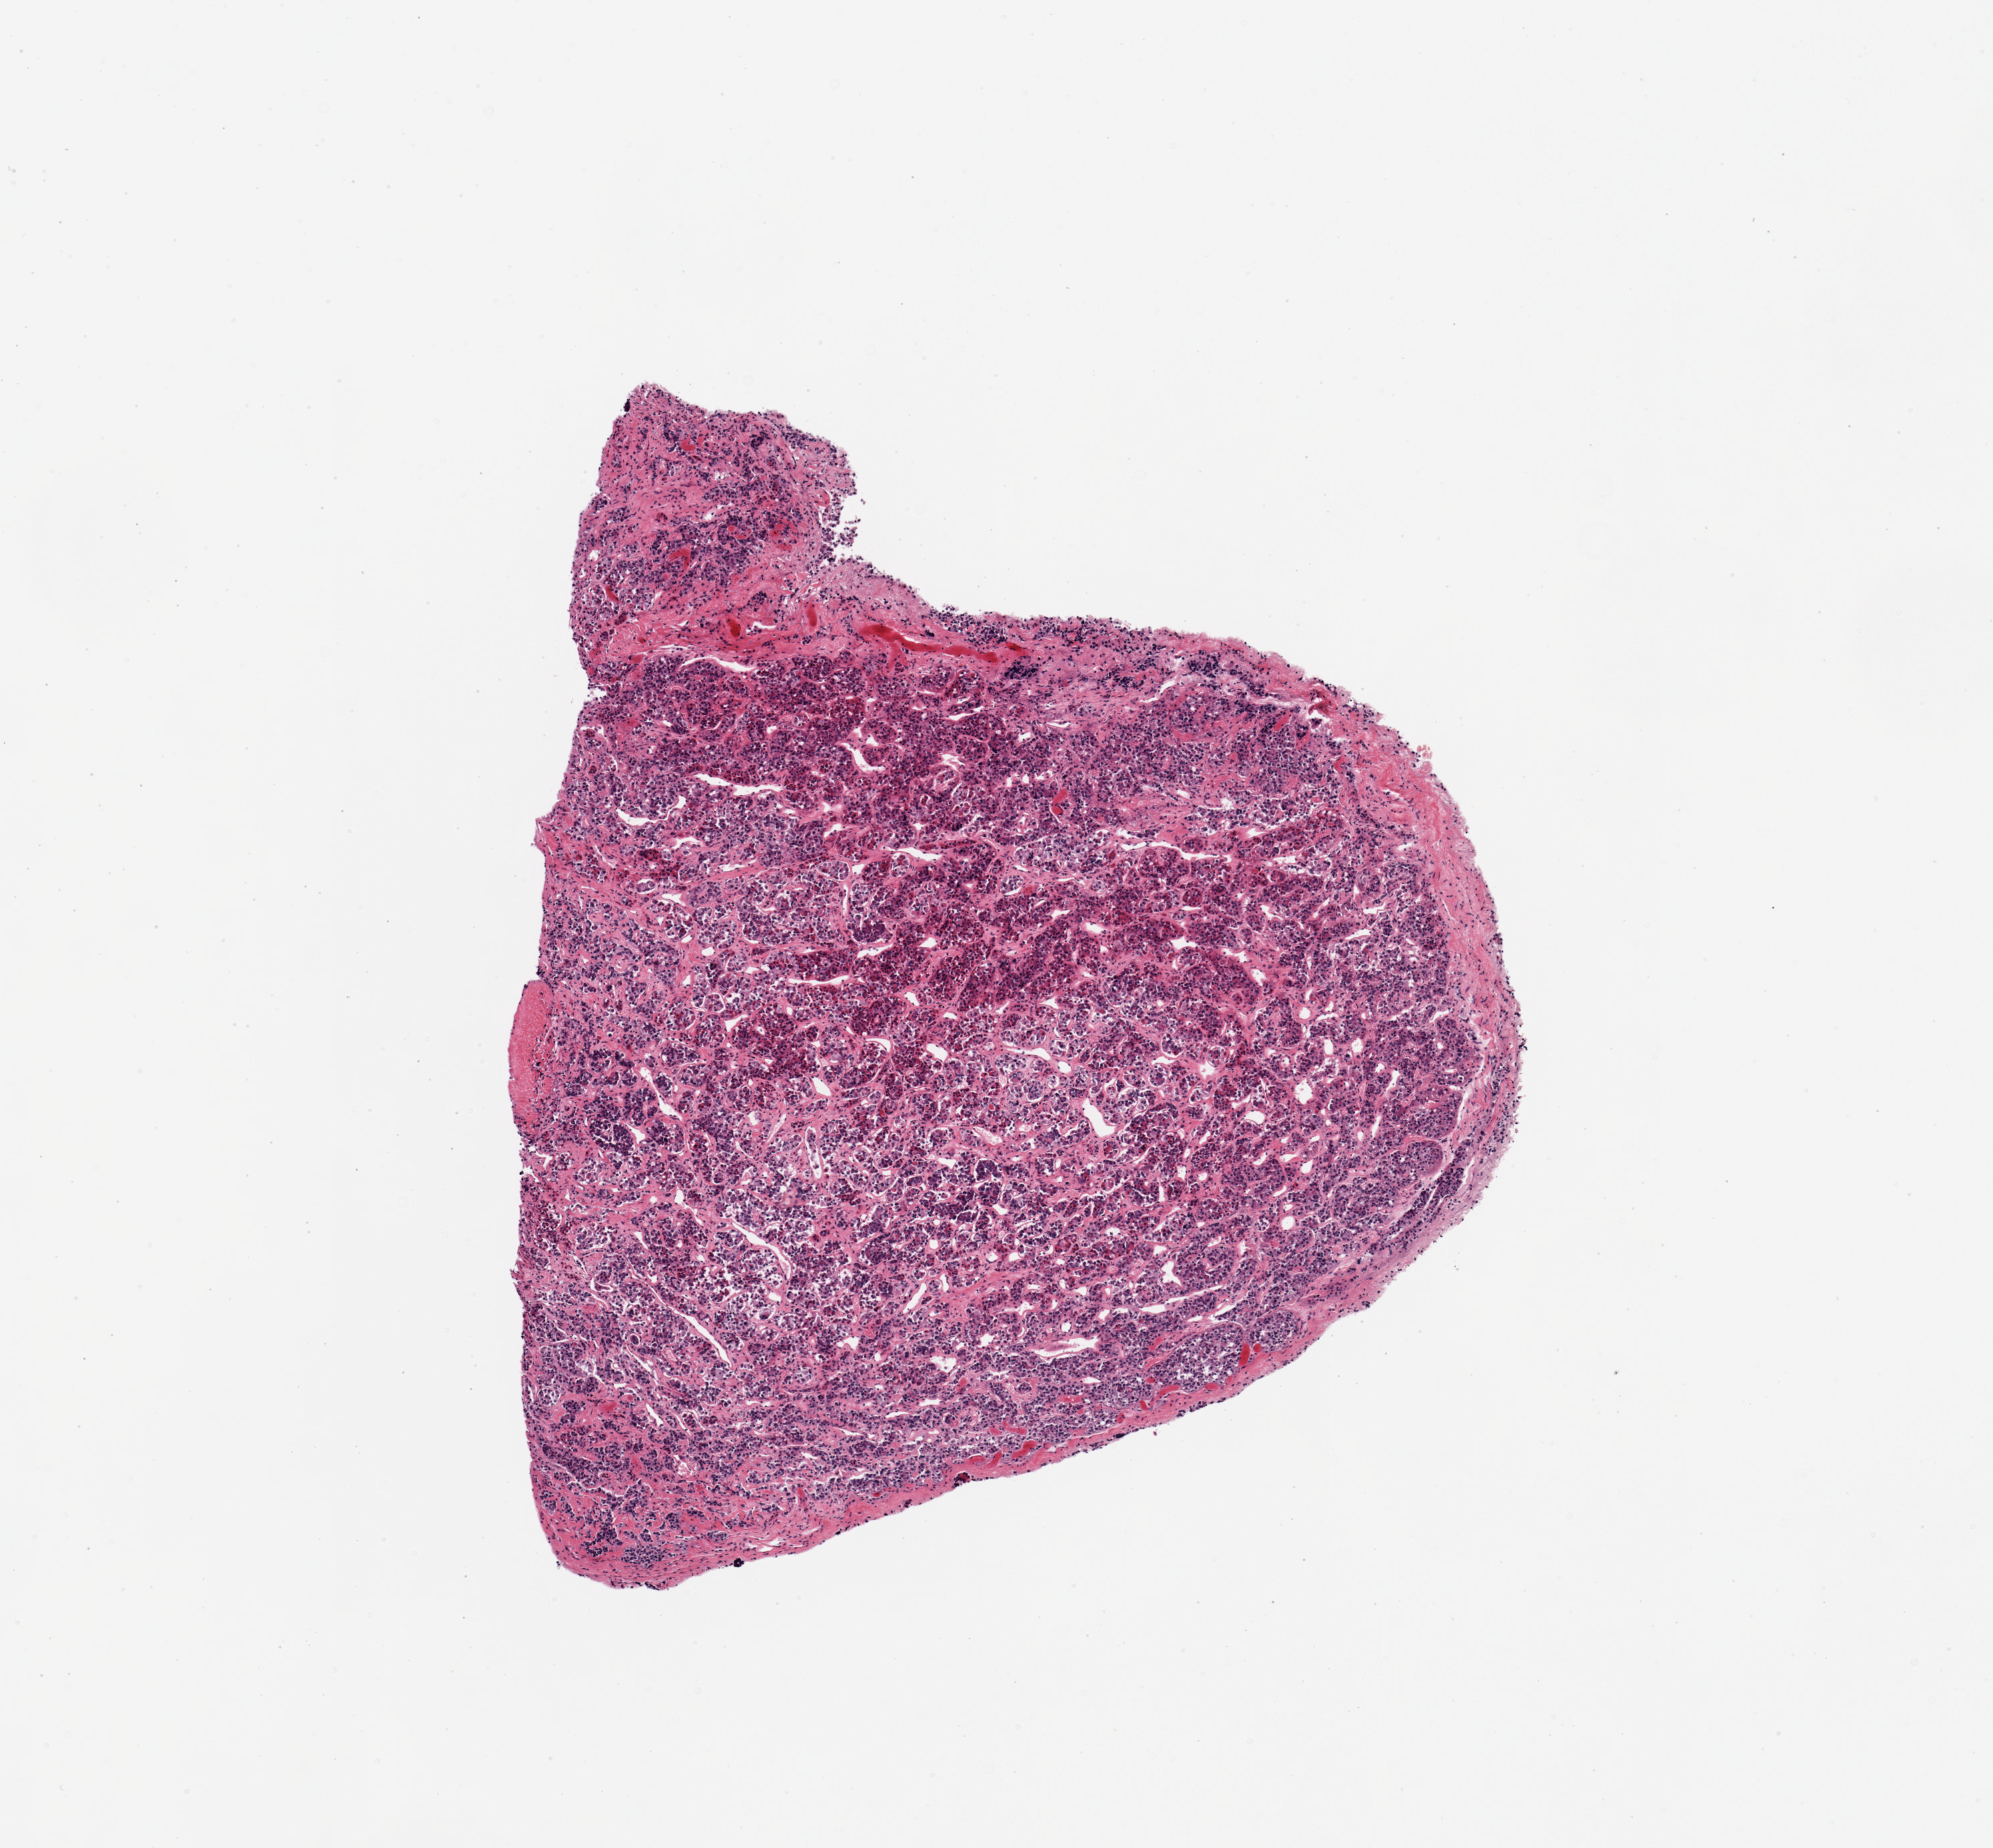
Hematoxylin and eosin (H&E) whole-slide image, shown as a low-resolution overview of the whole scanned area (about 5.9 x 5.5 mm). PAXgene-fixed paraffin-embedded (PFPE) section. Section of pituitary (target tissue). Tissue donor sample. Donor sex: male.
* review note (as recorded): 1 piece; adenohypophysis